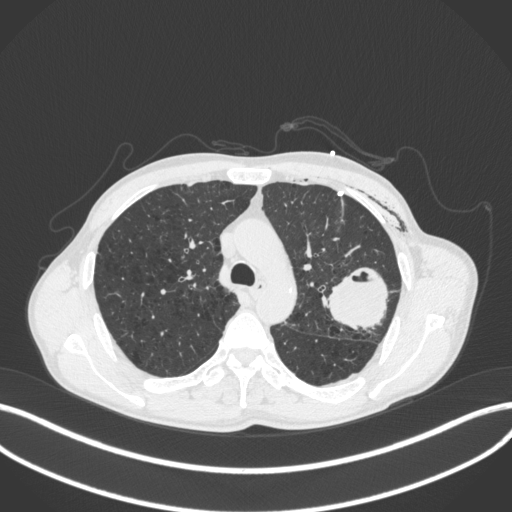
Chest CT, one axial slice; position 282 of 416 along the scan axis; reconstruction kernel B31f; 120 kVp; lung window (W 1500 / L -600 HU); 1 mm slice thickness; 512 × 512 image matrix, field of view 400 × 400 mm. Male patient, age 58 years. Case-level facts recorded for this patient, not image findings: clinical TNM (as recorded): T3 N0 M0.
Structures marked on this image (rectangle marked by the reading radiologist):
- lung tumour (recorded histology: adenocarcinoma): box from (x=326, y=263) to (x=395, y=334) px